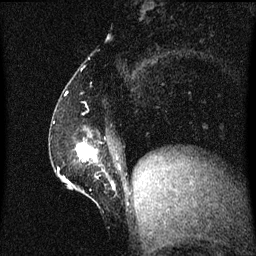
Breast MRI (dynamic contrast-enhanced), one sagittal slice. Slice 19 of 60 in the series (ordered by position). Dynamic contrast-enhanced series, image 2 of 3 at this slice position (ordered by acquisition). 1.5 T. TE 4.2 ms, TR 8.4 ms. 2 mm slice thickness. 256 × 256 image matrix, field of view 200 × 200 mm. Patient: female, 52 years. Case-level facts recorded for this patient, not image findings: setting: breast cancer imaged before/during neoadjuvant chemotherapy; receptor status: HER2-positive.
Annotated regions visible in this slice (semi-automatically segmented with operator editing):
- analysis volume of interest (the breast-tissue region the enhancement analysis was run in; not a lesion): bounding box <62,132,116,203> (left, top, right, bottom; pixels)
- tumour enhancement mask (voxels above the 70 % enhancement threshold inside the analysis volume of interest): <77,142,115,187>